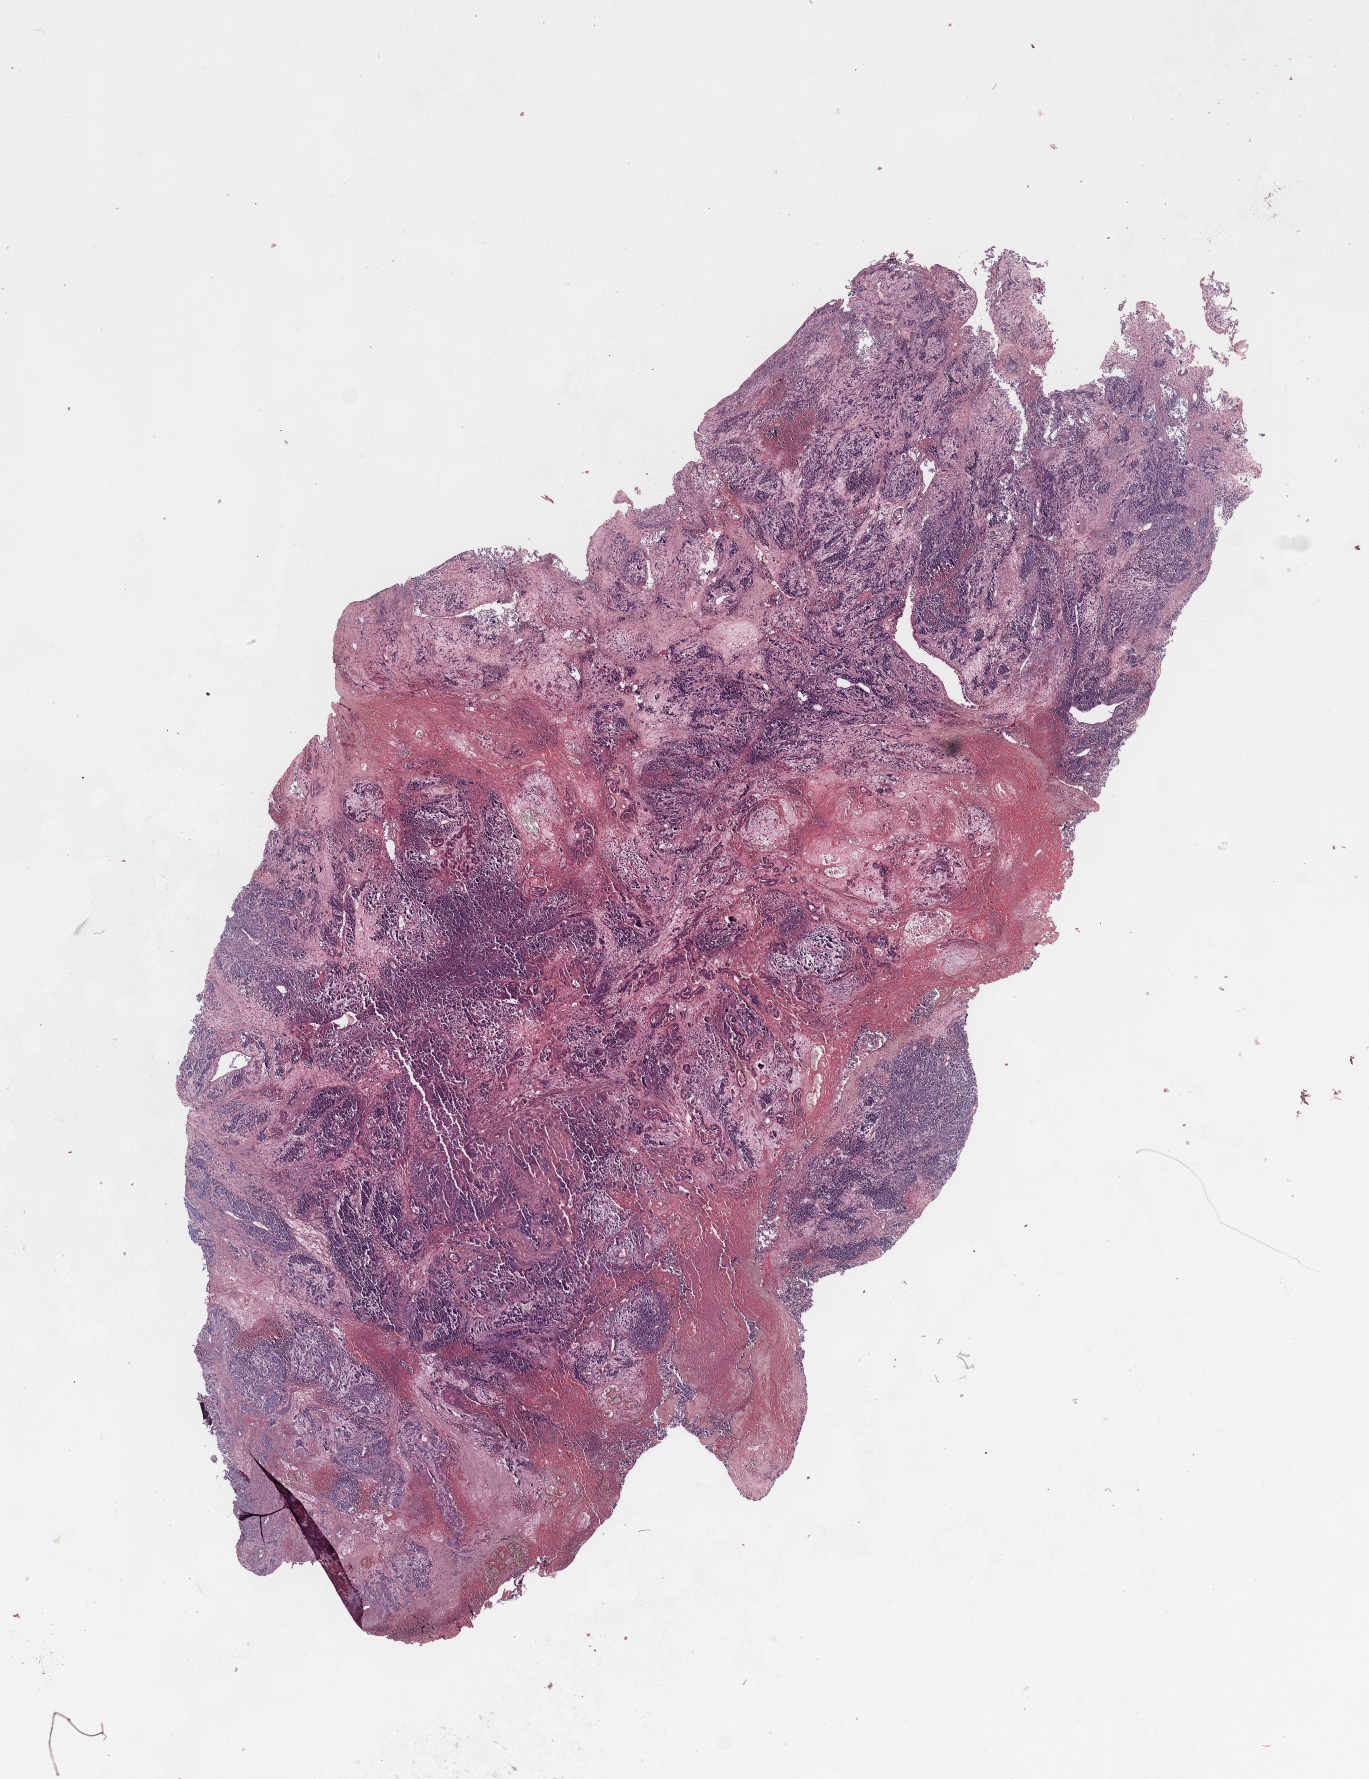
Whole-slide histology image, H&E, a low-resolution overview of the entire scanned area, about 10.8 x 14.1 mm (slide scanned at 20x). Uterus, tumour tissue. Patient: female, age 68 years.
Histologic diagnosis: Endometrioid adenocarcinoma, NOS.